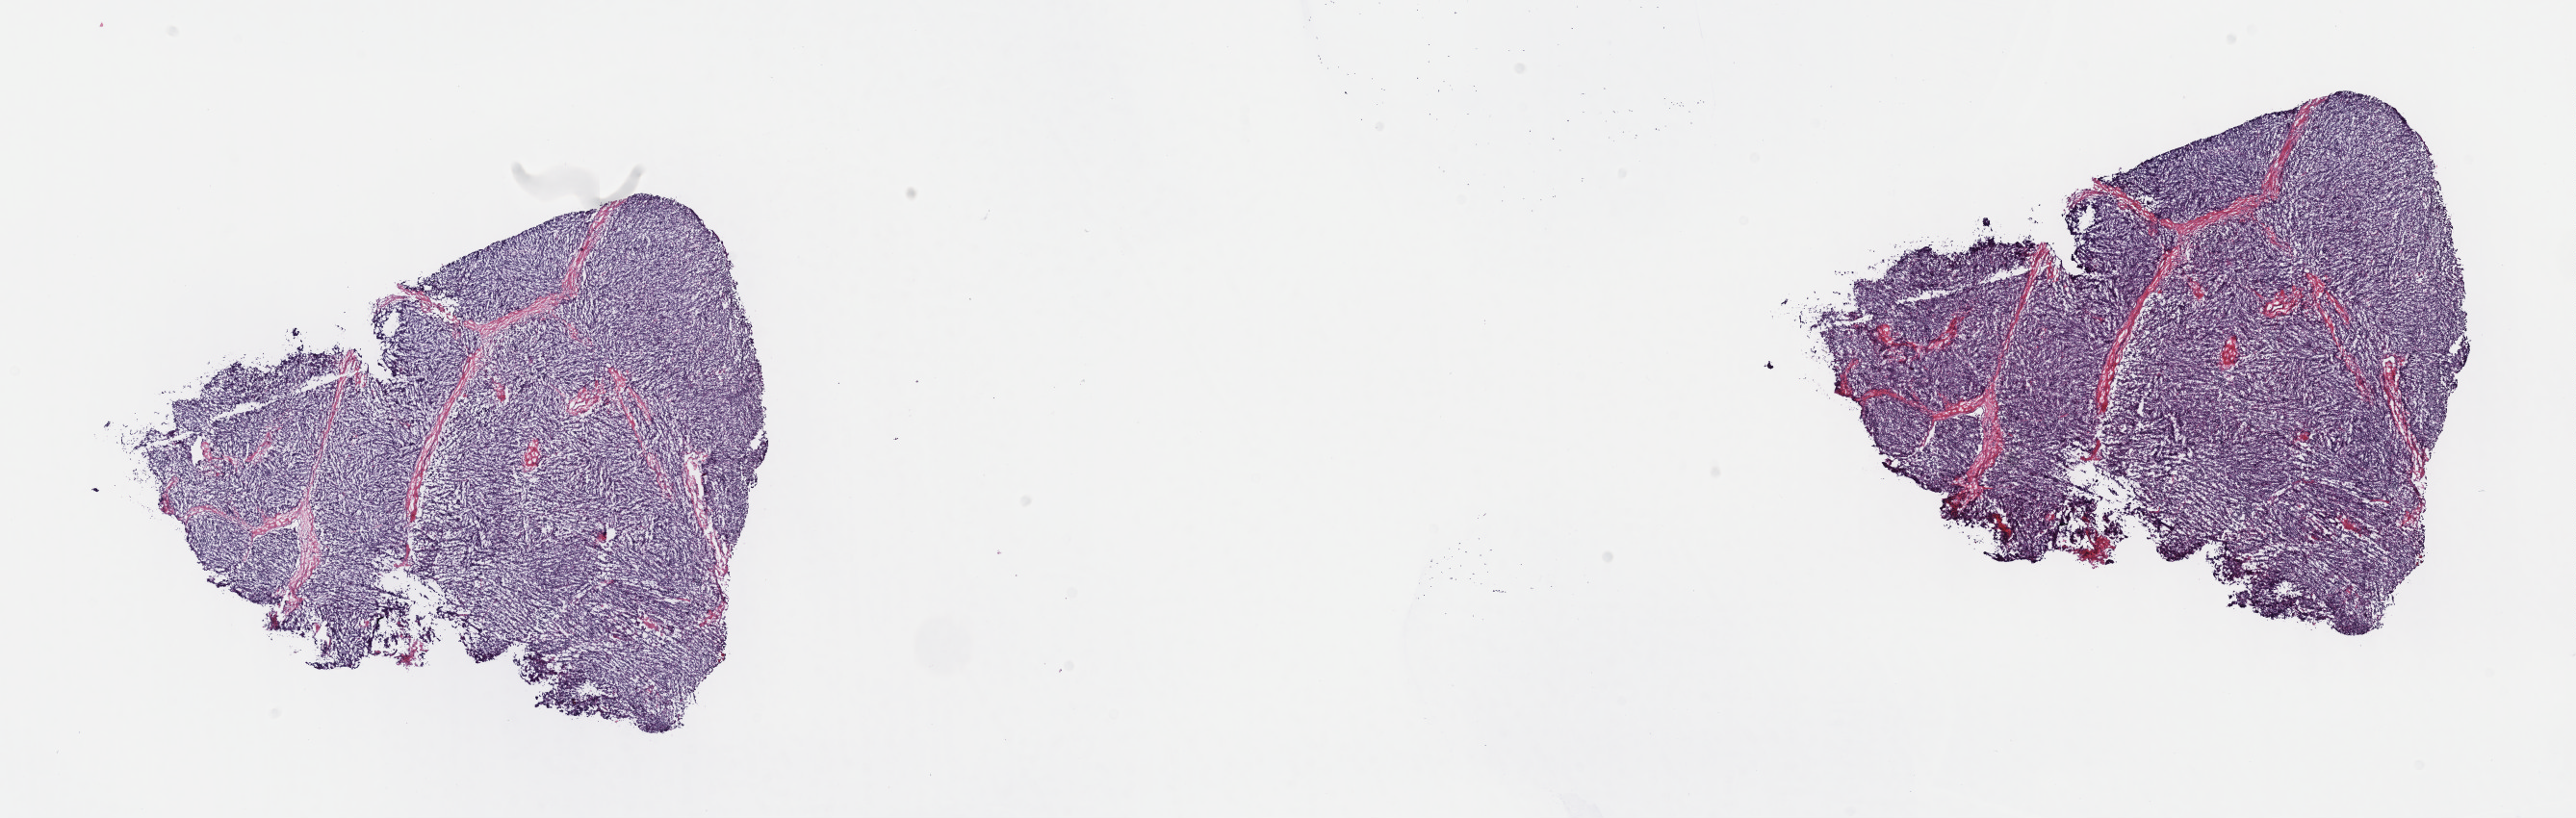
H&E-stained whole-slide image — low-resolution overview of the scanned area, about 21.6 x 6.9 mm (from a 40x scan); frozen section from the top of the tissue portion; thymus, primary tumour sample. Patient: male, age at initial diagnosis 39 years. Slide review estimates, as recorded: tumour cells 90%, tumour nuclei 95%.
Histologic diagnosis: Thymoma, type B2, malignant.